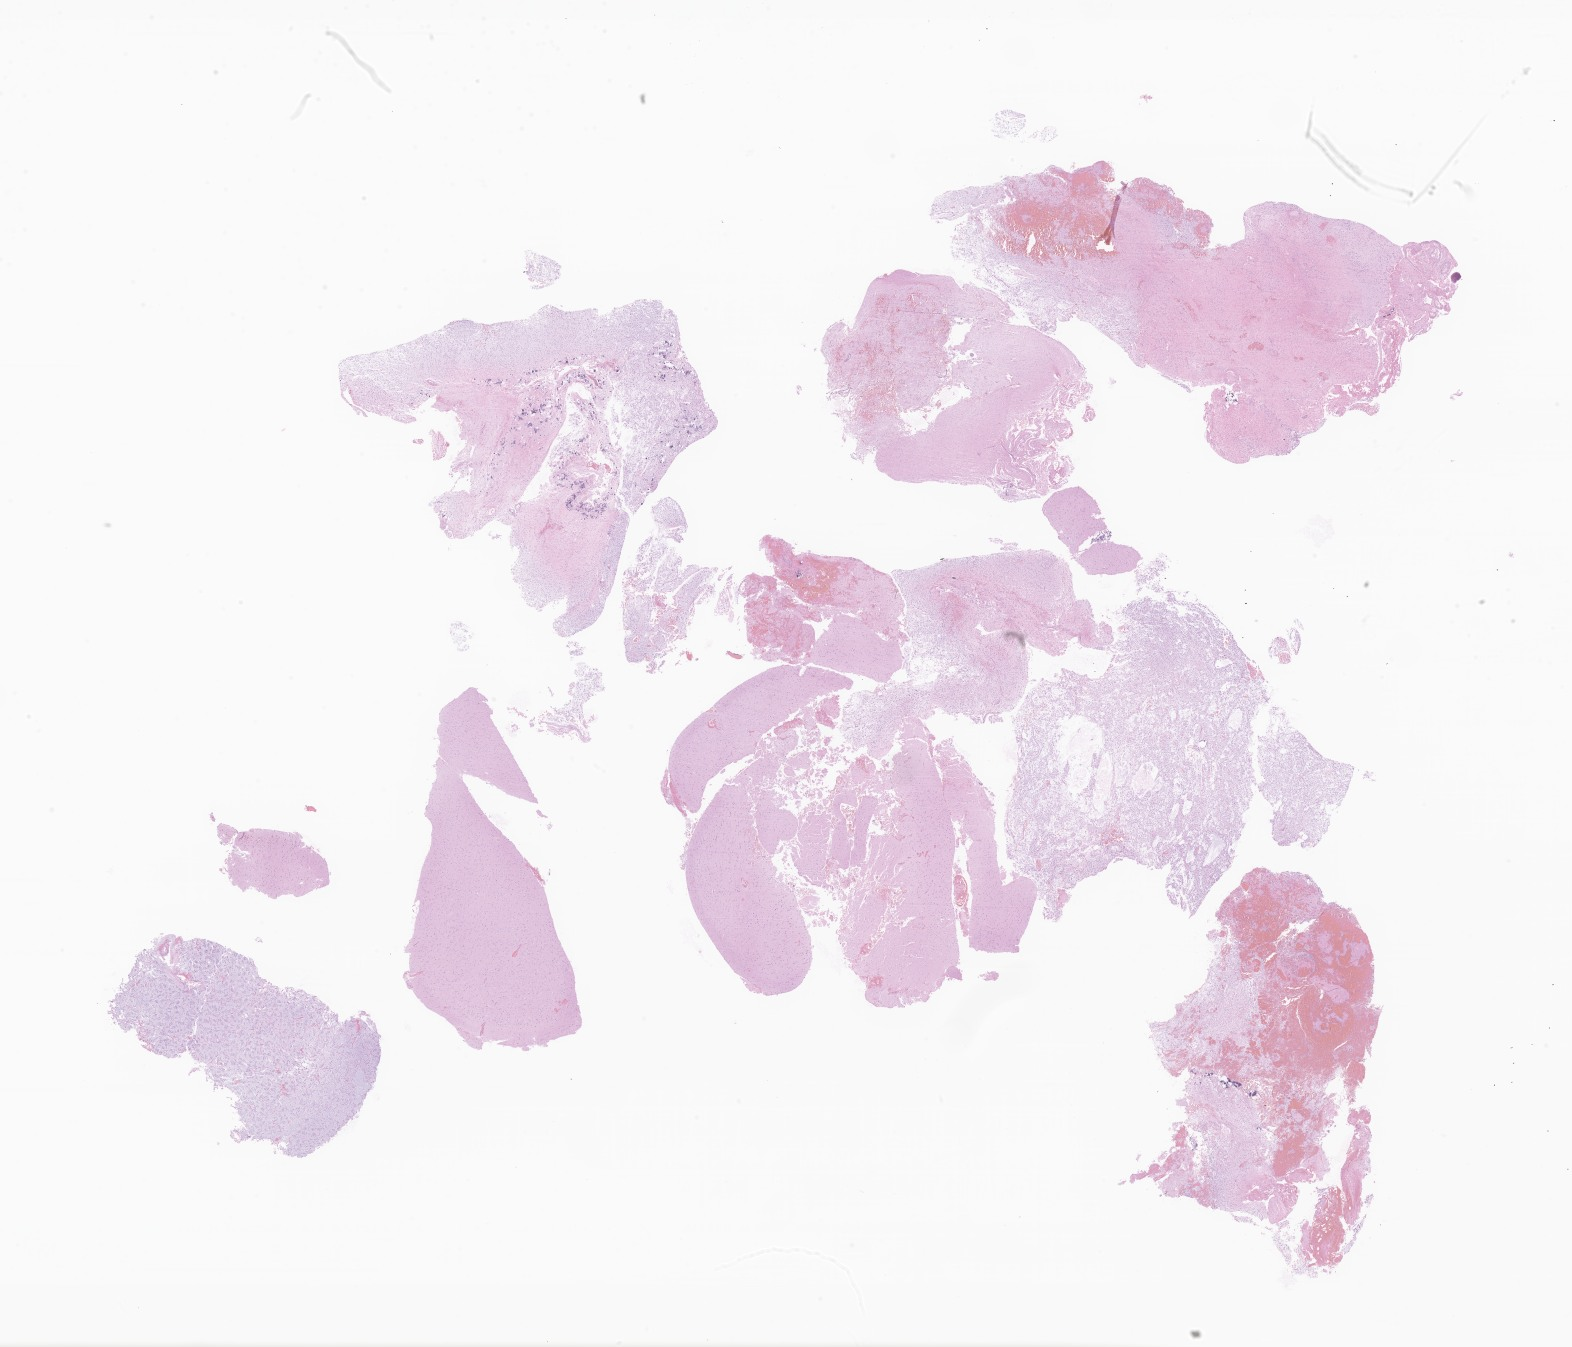
Whole-slide image, haematoxylin and eosin stain of tumor tissue from the brain, low-resolution overview of the scanned area, about 26.5 x 22.7 mm. Formalin-fixed paraffin-embedded section. Patient: female, age 217 months (18 years 1 month).
• recorded diagnosis: Neoplasm, uncertain whether benign or malignant